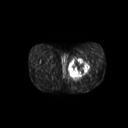
FDG PET of an extremity soft-tissue mass (from a PET/CT study), one axial slice. Slice 32 of 267 in the series (ordered by position). 128 × 128 image matrix. Patient: male, 59 years. Case-level facts recorded for this patient, not image findings: histological type: pleiomorphic liposarcoma; grade: high; site of the primary tumour: left thigh.
Annotated regions visible in this slice (expert contour drawn on MRI and transferred to this co-registered scan by the dataset authors):
- gross tumour volume including surrounding oedema: box from (x=69, y=58) to (x=90, y=78) px
- gross tumour volume (mass): (x=69, y=58)–(x=89, y=77)